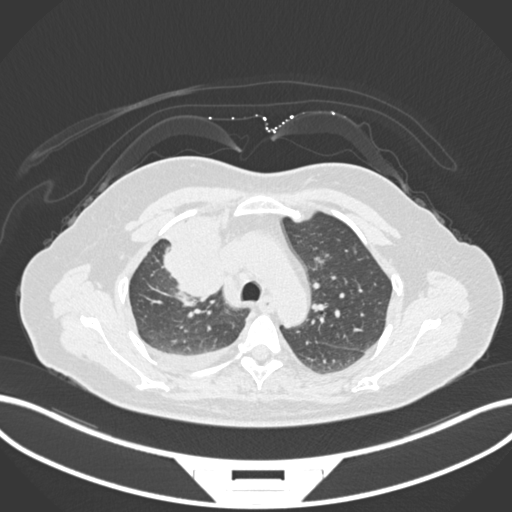
Chest CT, one axial slice. Slice 113 of 172 in the series (ordered by position). Reconstruction kernel B30f. 120 kVp. Lung window (W 1500 / L -600 HU). 1 mm slice thickness. 512 × 512 image matrix, field of view 400 × 400 mm. Patient: female, 52 years. From the clinical record (not read from this slice): clinical TNM (as recorded): T3 N1 M1.
Structures marked on this image (bounding box drawn by a radiologist):
- lung tumour (recorded histology: adenocarcinoma): bounding box [x1, y1, x2, y2] px = [156, 206, 226, 303]